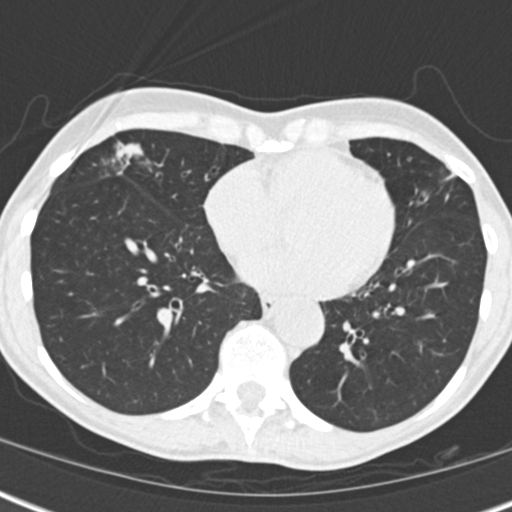
Low-dose screening chest CT, one axial slice. Position 66 of 173 along the scan axis. Reconstruction kernel B30f. 120 kVp. Lung window (W 1500 / L -600 HU). 2 mm slice thickness. 512 × 512 image matrix, field of view 290 × 290 mm.
Outlined on this slice (expert manual segmentation):
- lesion 1 (tumor, middle lobe of right lung): bounding box (x1, y1, x2, y2) in pixels: (118, 144, 141, 157)